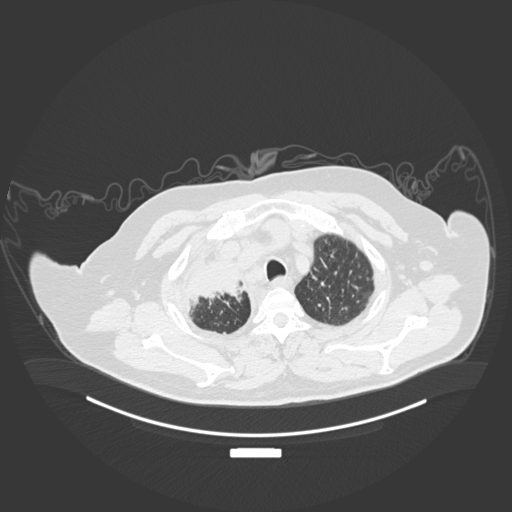
Chest CT, one axial slice; slice 162 of 201 in the series (ordered by position); 120 kVp; lung window (W 1500 / L -600 HU); 1 mm slice thickness; 512 × 512 image matrix. Male patient, age 69 years. Case-level facts recorded for this patient, not image findings: clinical TNM (as recorded): T4 N3 M1.
Outlined on this slice (bounding box drawn by a radiologist):
- lung tumour (recorded histology: adenocarcinoma): bounding box <186,261,242,304> (left, top, right, bottom; pixels)